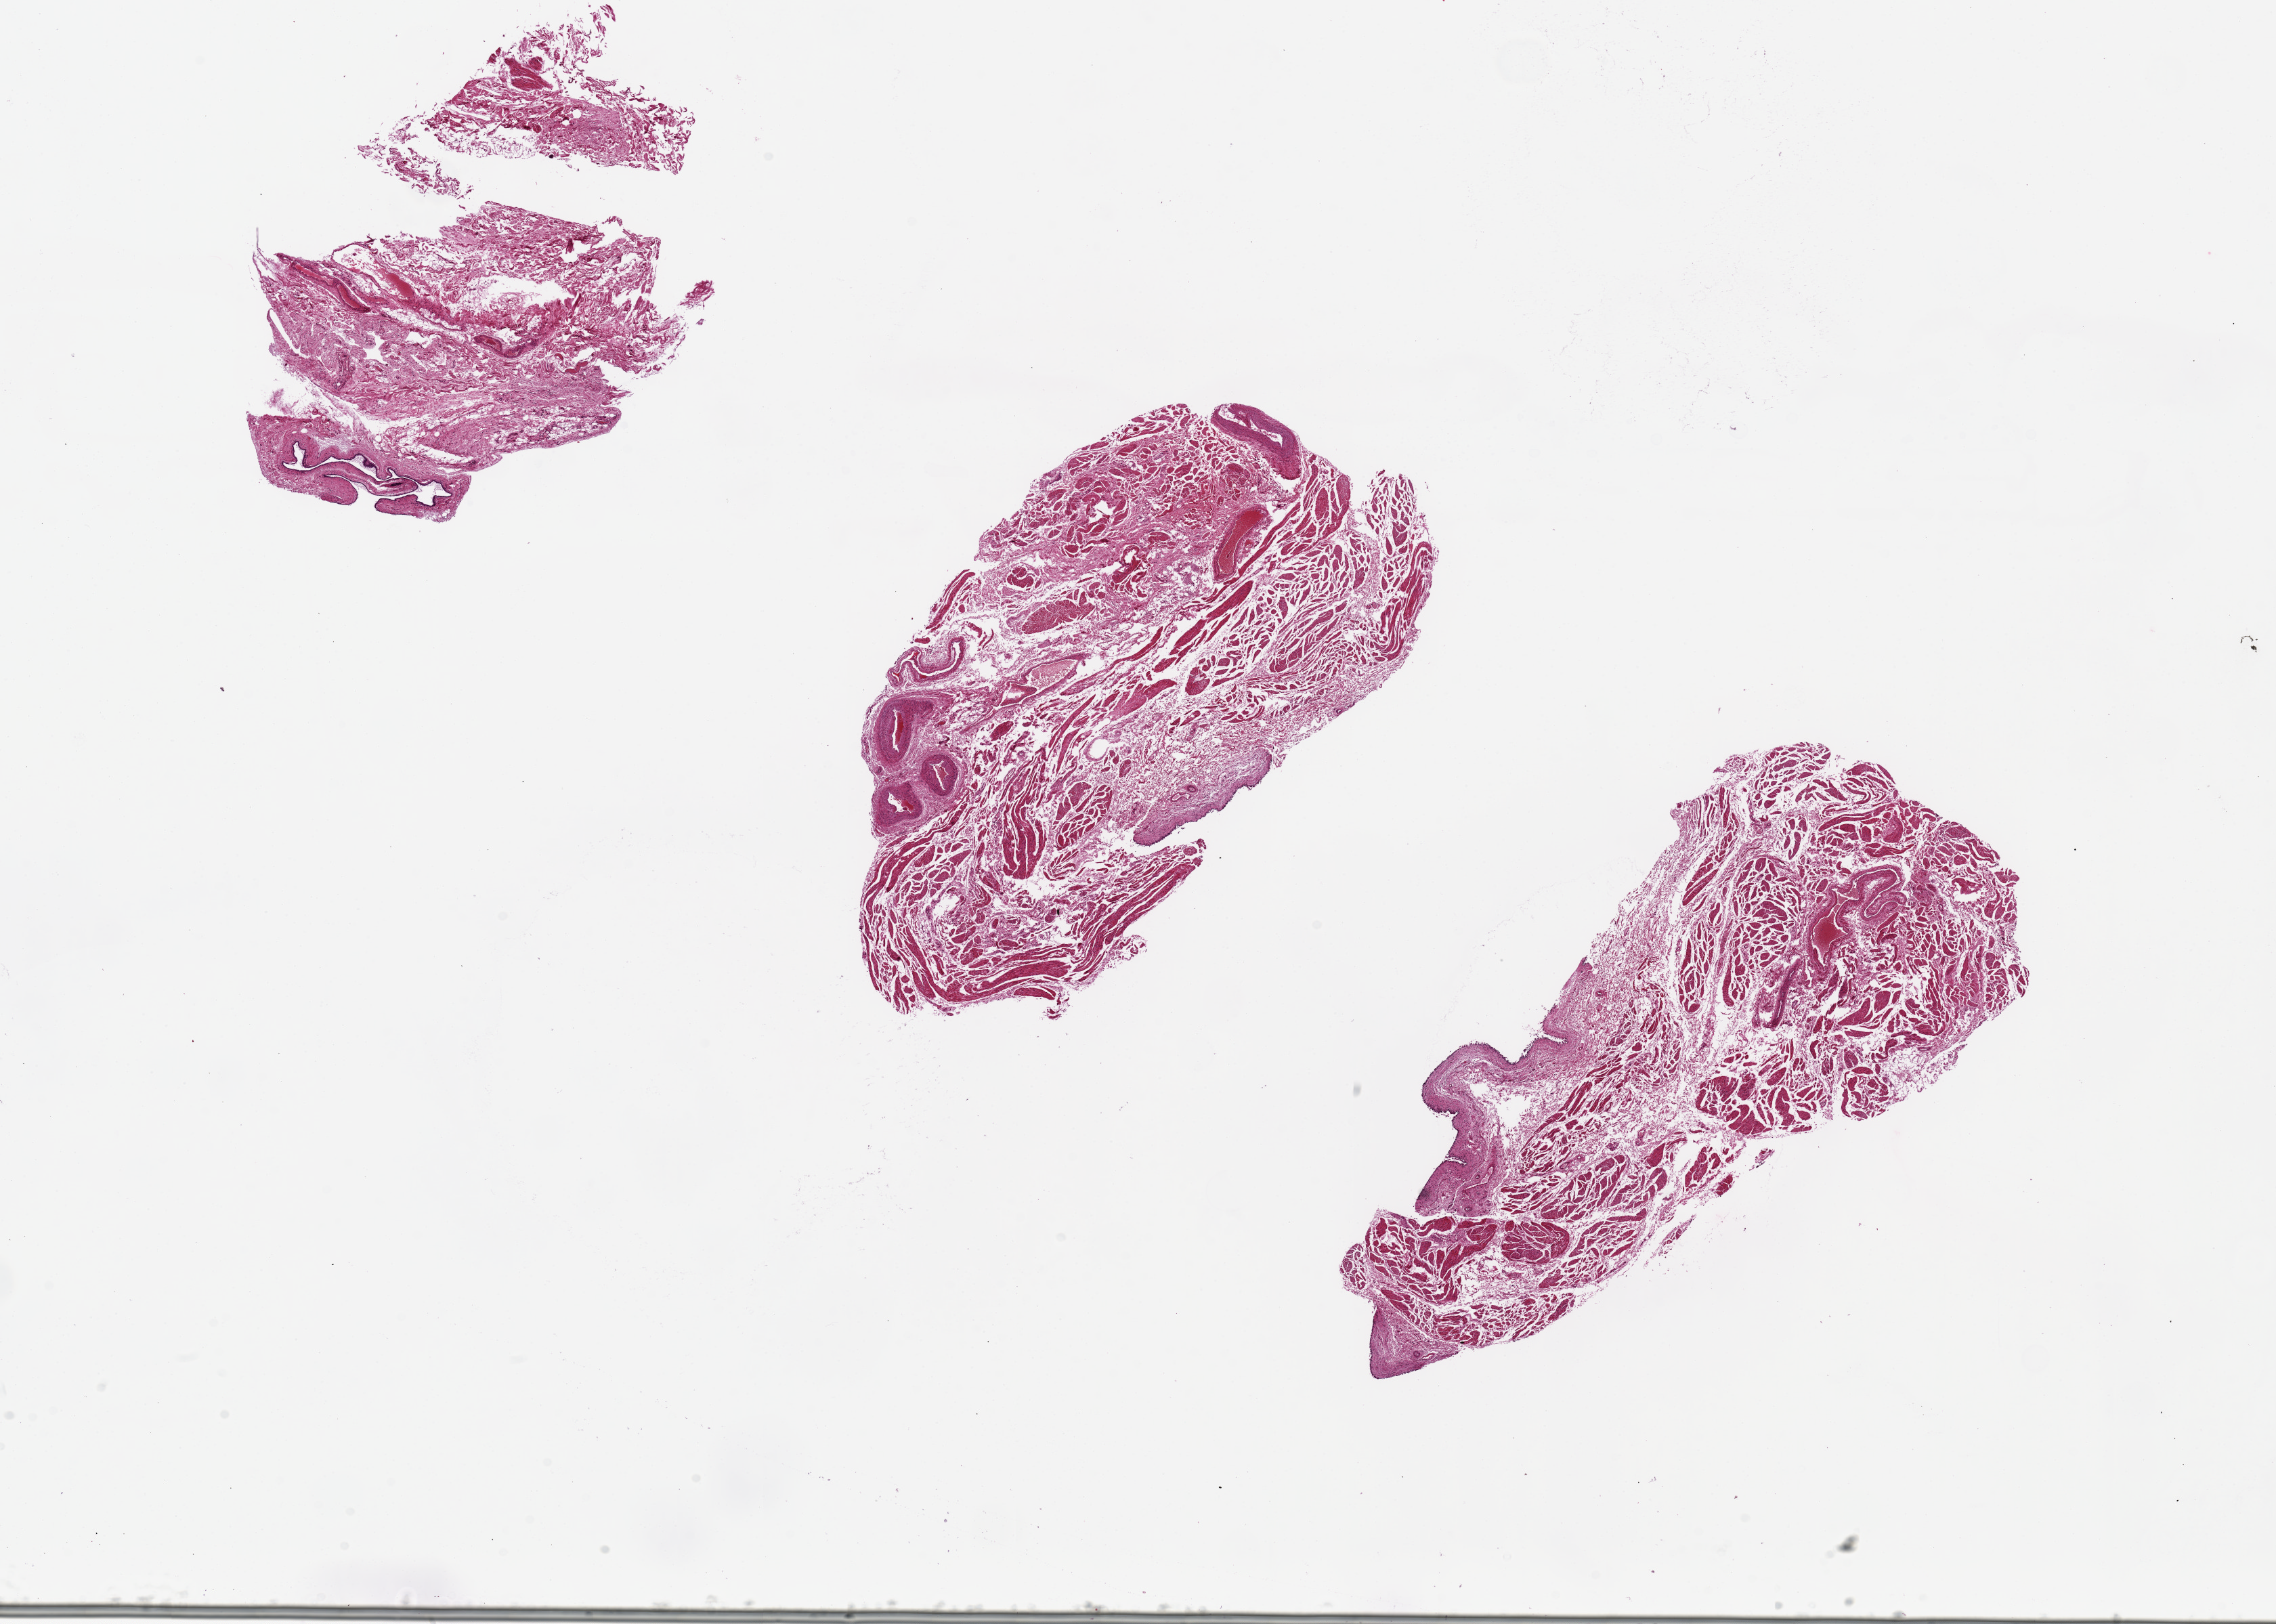
Whole-slide image, haematoxylin and eosin stain, low-resolution overview of the scanned area, about 26.6 x 19.0 mm (acquisition: 20x scan); PAXgene-fixed, paraffin-embedded tissue; target tissue: urinary bladder; tissue donor sample. Donor sex: female.
Review note (as recorded): 3; most epithelium sloughed.